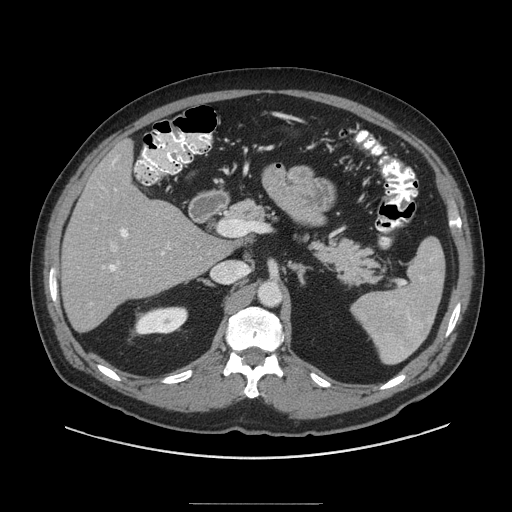
Contrast-enhanced abdominal CT (liver protocol), one axial slice. Slice 52 of 91 in the series (ordered by position). Reconstruction kernel STANDARD. 140 kVp. Soft-tissue window (W 400 / L 40 HU). 512 × 512 image matrix, field of view 440 × 440 mm. From the clinical record (not read from this slice): diagnosis: hepatocellular carcinoma (patient treated with transarterial chemoembolisation; whether this scan precedes or follows treatment is not stated here); TNM stage (as recorded): Stage-I; Child-Pugh class: A; tumour nodularity: uninodular; tumour size: 4 cm.
Outlined on this slice (semi-automatically segmented with operator editing):
- liver parenchyma outside the tumour (the mass and vessels are separate outlines, so this box may not span the whole liver): bounding box <60,140,230,330> (left, top, right, bottom; pixels)
- liver vessels: <102,158,164,272>